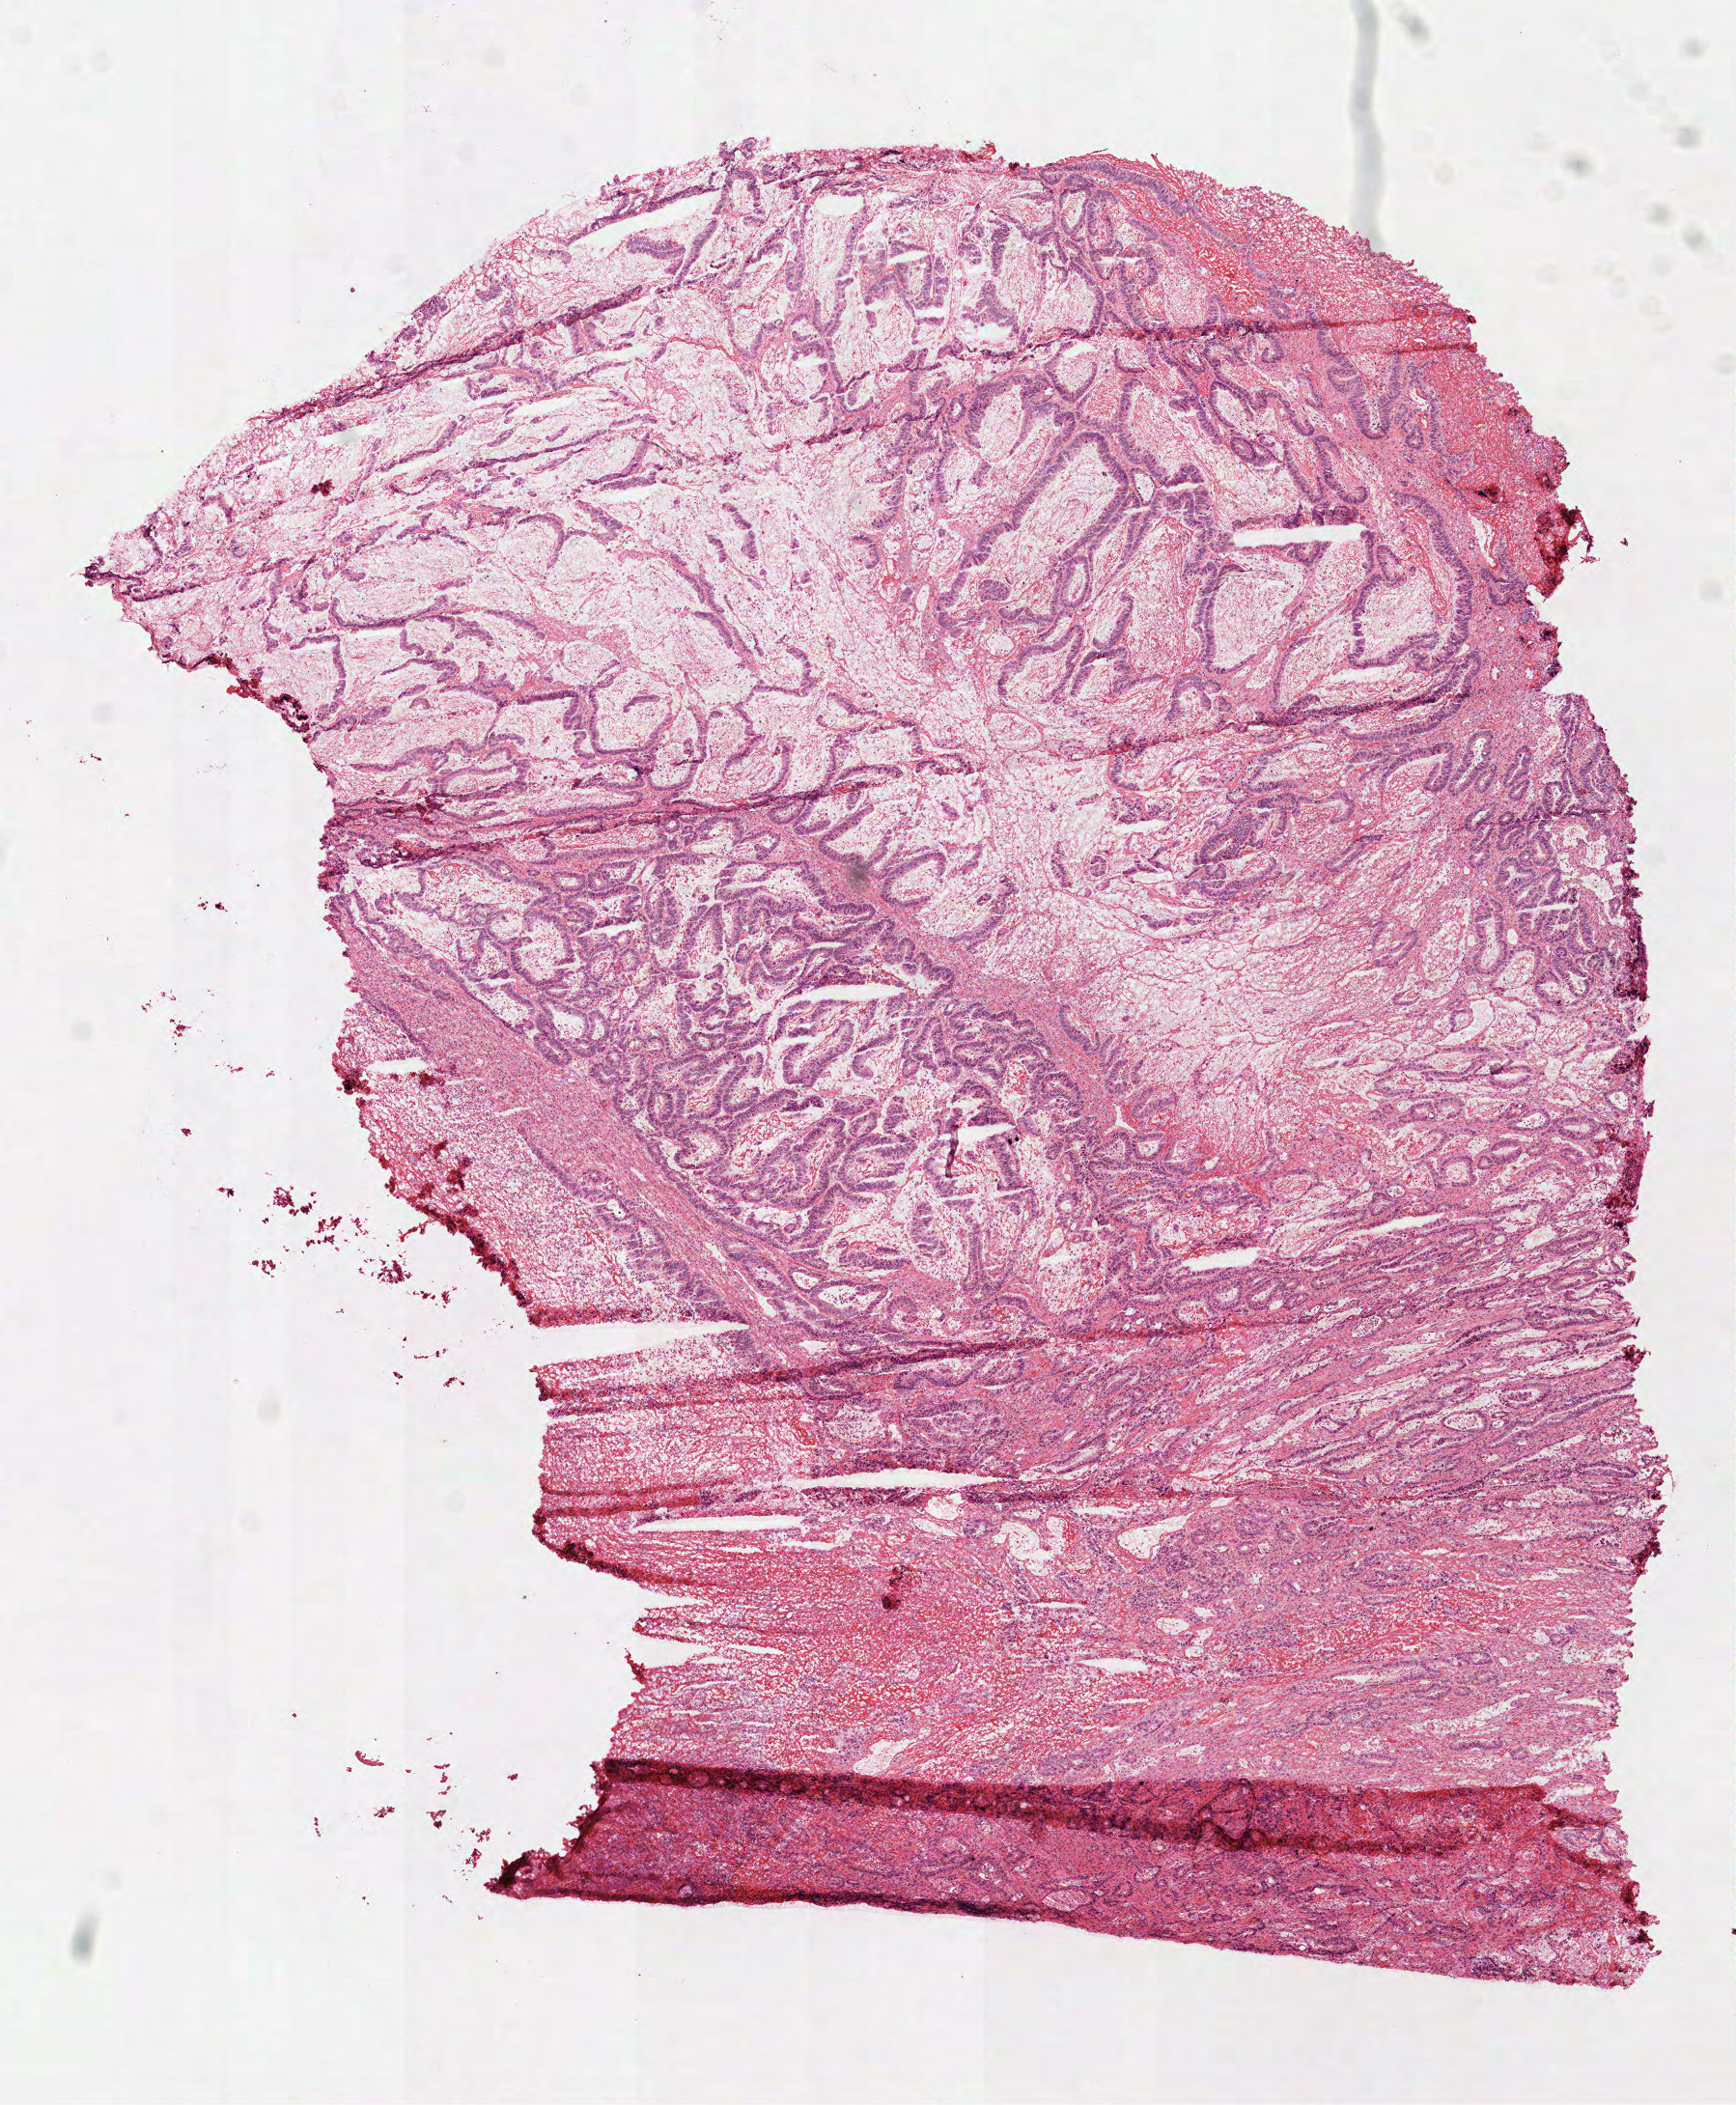
H&E whole-slide image — low-resolution overview of the scanned area, about 7.3 x 8.8 mm. Frozen section from the top of the tissue portion. Colon, primary tumour sample. Male, age 73 years at initial diagnosis. Slide review estimates, as recorded: tumour cells 95%, tumour nuclei 80%, normal cells 0%, stromal cells 0%, necrosis 5%. Inflammatory infiltration, as recorded: lymphocyte infiltration 7%, monocyte infiltration 2%, neutrophil infiltration 7%.
* lymph nodes positive (case pathology): 0 of 14 examined
* diagnosis: Adenocarcinoma, NOS
* AJCC pathologic stage: IIA (7th edition)